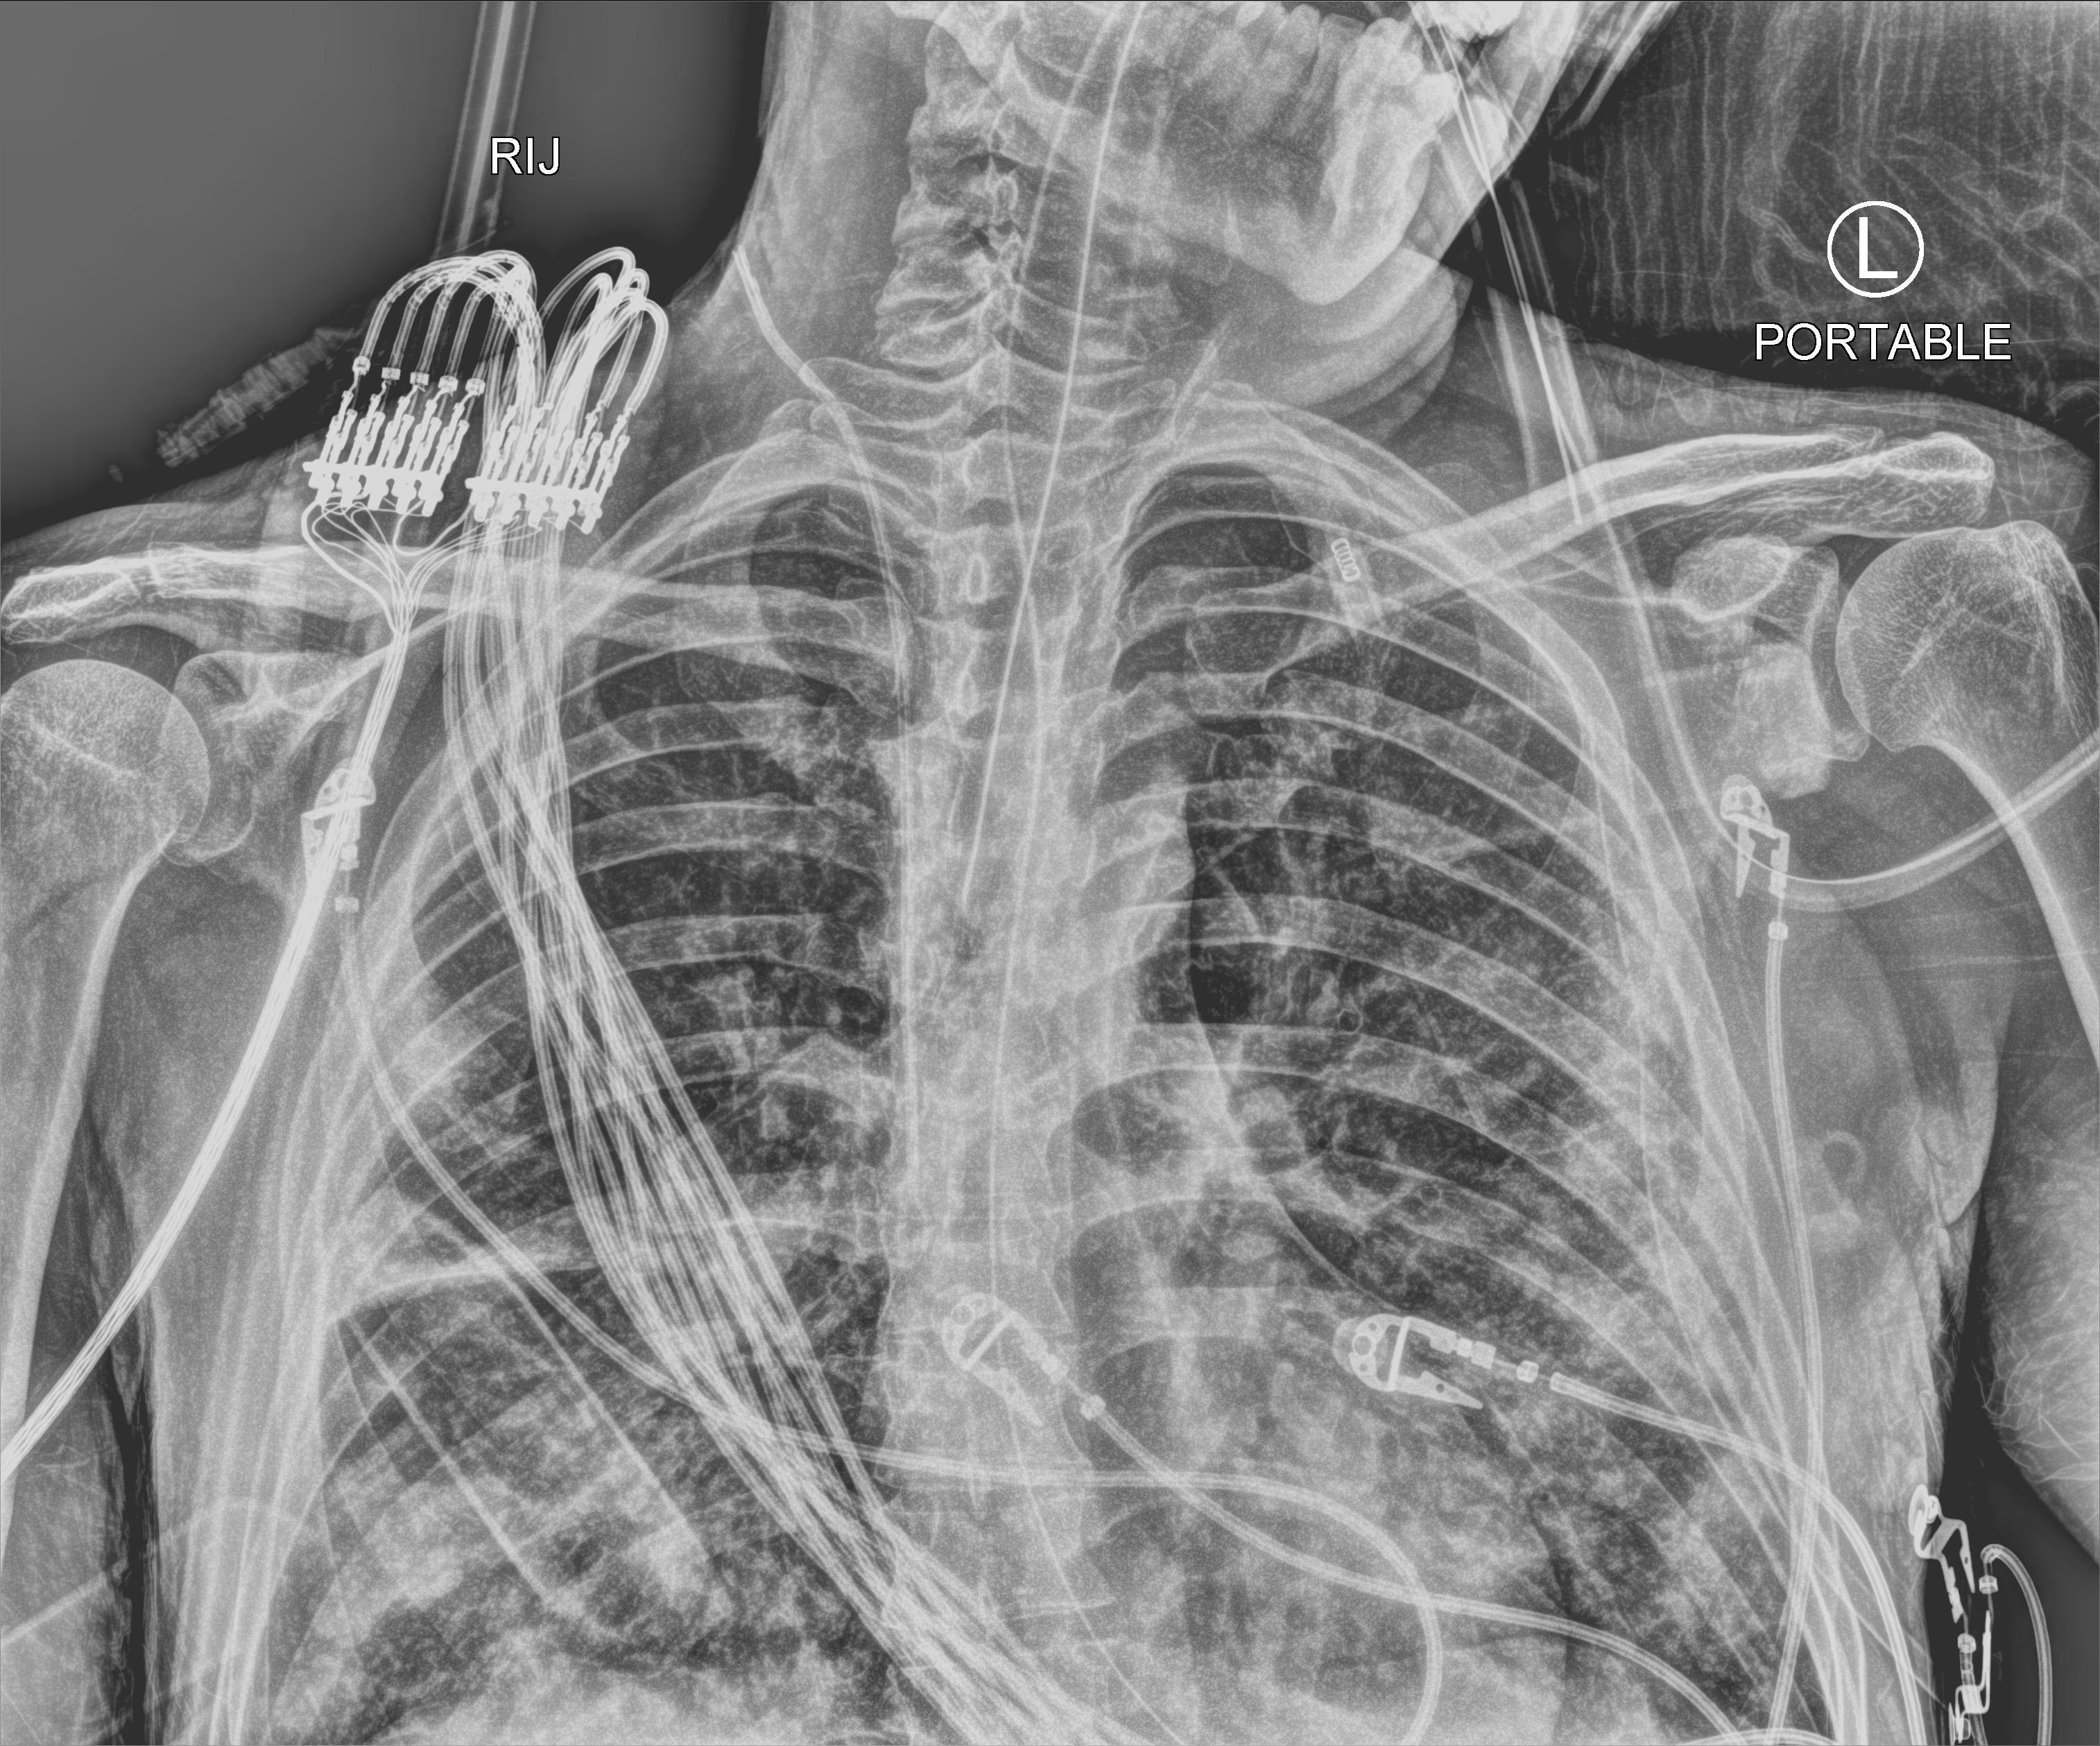
Chest X-ray (portable); anteroposterior (AP) projection. Male patient hospitalised with COVID-19, age 18–59 years.
Hospital-stay facts (about this admission, not read from this image; timing relative to this image not recorded): chronic kidney disease (admission record): no.